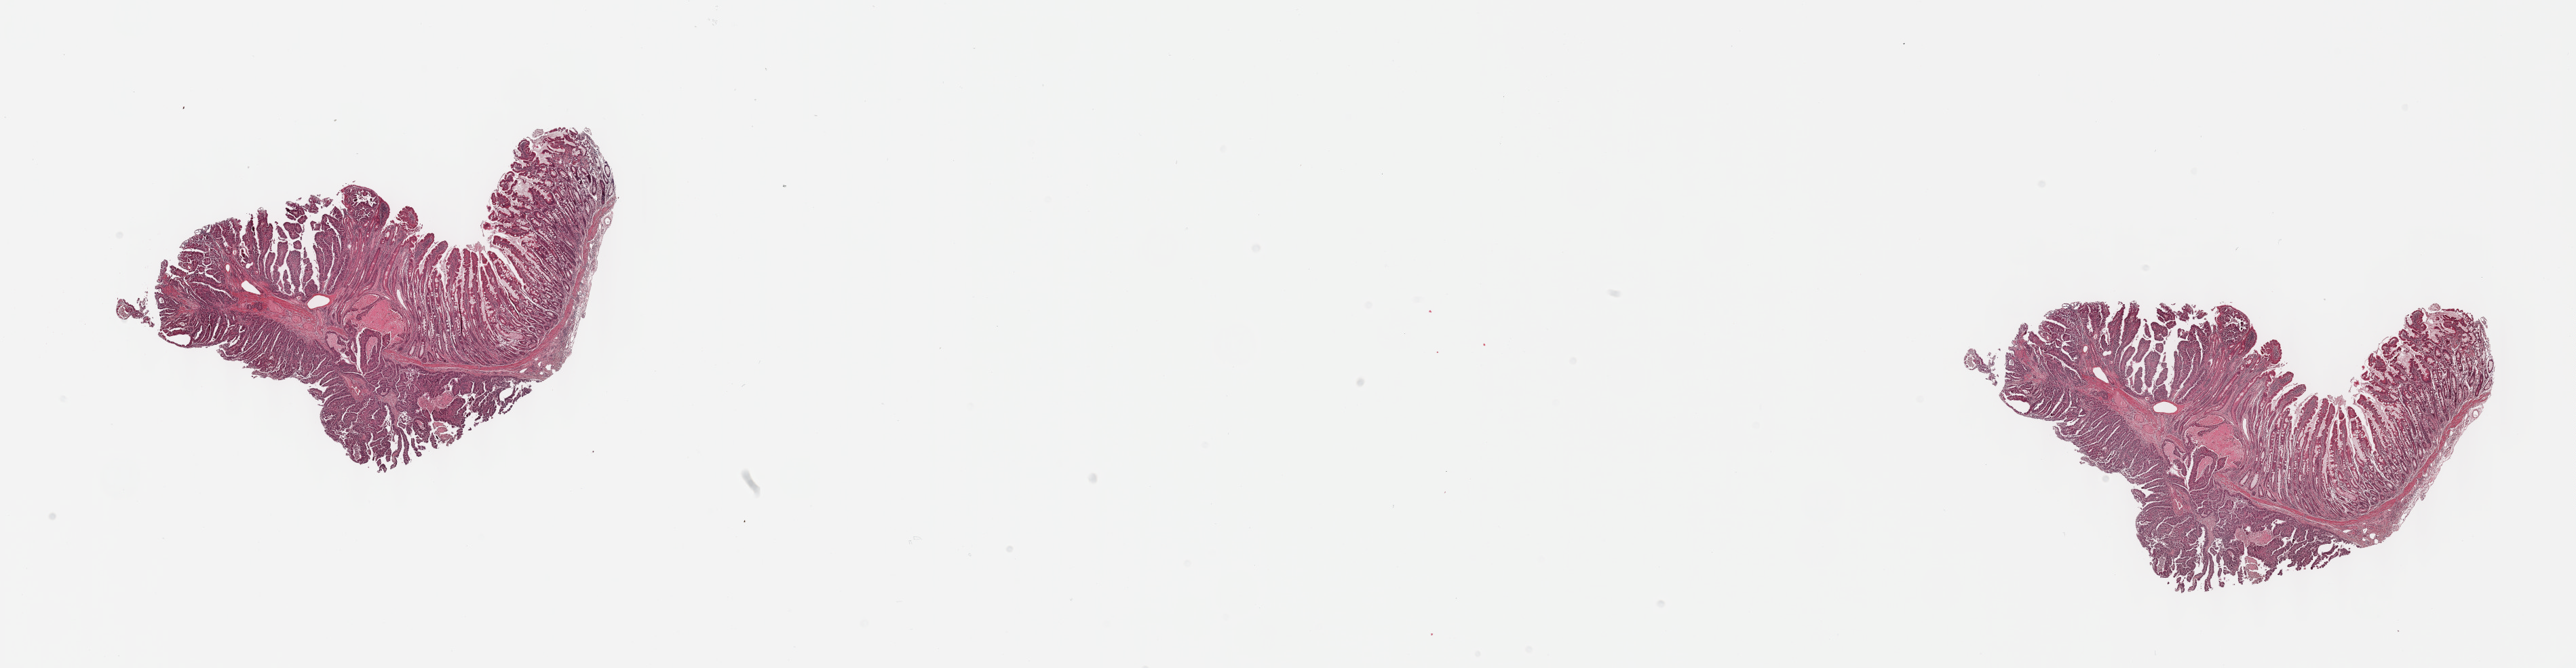
Hematoxylin and eosin (H&E) stained whole-slide image — a low-resolution overview of the entire scanned area, about 30.7 x 8.0 mm. FFPE section. Sample: primary tumour, pancreas. Male patient; age at initial diagnosis 72 years. Histologic grade: GX (grade cannot be assessed).
- pathologic diagnosis: Infiltrating duct carcinoma, NOS (head of pancreas)
- AJCC pathologic stage: IIB (7th edition)
- lymph nodes positive (case pathology): 7 of 28 examined